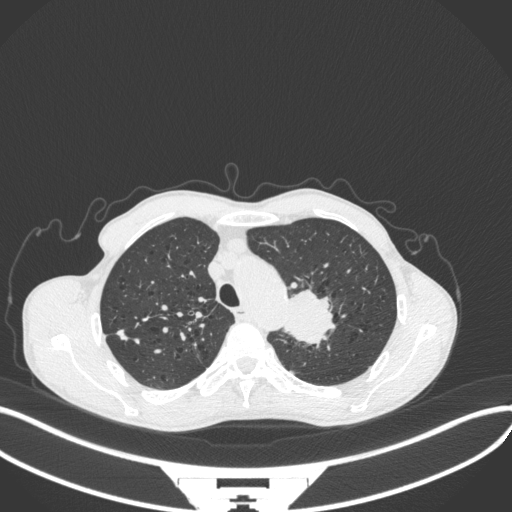
Chest CT, one axial slice; lung window (W 1500 / L -600 HU); 1 mm slice thickness; 512 × 512 image matrix, field of view 400 × 400 mm. Patient: male, 65 years. From the clinical record (not read from this slice): clinical TNM (as recorded): T2b N0 M0; histopathological grade: G2.
Structures marked on this image (rectangle marked by the reading radiologist):
- lung tumour (recorded histology: adenocarcinoma): box from (x=279, y=282) to (x=340, y=344) px